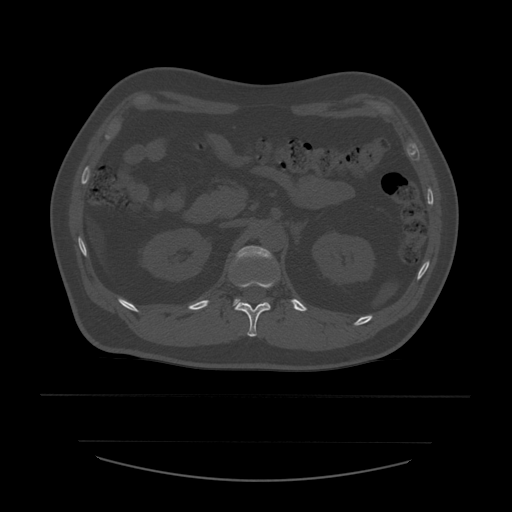
CT including the spine, one axial slice; slice 242 of 532 in the series (ordered by position); 120 kVp; bone window (W 1800 / L 400 HU); 1.25 mm slice thickness; 512 × 512 image matrix, field of view 441 × 441 mm. Patient age 44 years. From the clinical record (not read from this slice): primary cancer: soft tissue sarcoma.
Outlined on this slice (semi-automatically segmented with operator editing):
- L1 vertebra: bounding box [x1, y1, x2, y2] px = [234, 246, 275, 306]
- T12 vertebra: [235, 278, 278, 337]